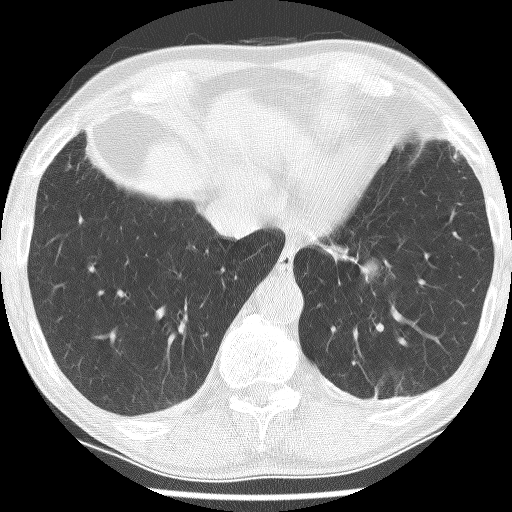
Axial slice from a low-dose chest CT screening exam, baseline annual screen, lung window (W 1500 / L -600 HU), 2.5 mm slice thickness. Male participant, aged 74 years at enrolment. Current smoker at enrolment.
Expert-annotated lung lesion, bounding box (x1, y1, x2, y2) in pixels: (310, 211, 409, 304). Reader record for this screening exam (exam-level; its link to the box is not recorded): non-calcified nodule or mass ≥4 mm, left lower lobe, 30 × 27 mm, spiculated (stellate) margins, soft tissue attenuation. Official screen result: positive, change unspecified: nodule(s) >= 4 mm or enlarging nodule(s), mass(es), or other non-specific abnormalities suspicious for lung cancer. Lung cancer was diagnosed 151 days after this screen: adenocarcinoma, NOS, left lower lobe, stage IIIA (AJCC 6th edition), 49 mm at pathology.